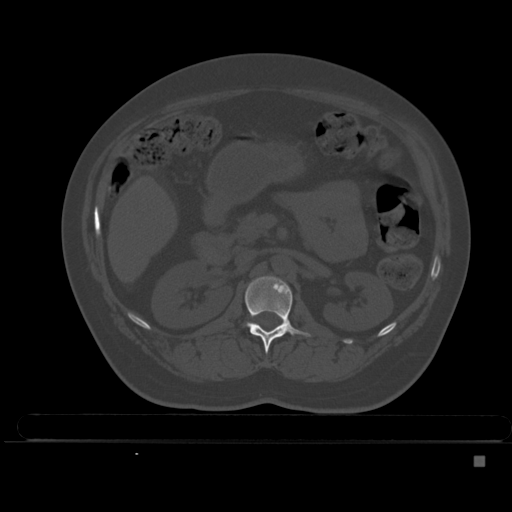
CT including the spine, one axial slice. Position 192 of 495 along the scan axis. Bone window (W 1800 / L 400 HU). 1.5 mm slice thickness. 512 × 512 image matrix. Female patient, age 33 years. From the clinical record (not read from this slice): primary cancer: breast; vertebrae with lytic lesions (as recorded): T1.
Annotated regions visible in this slice (semi-automatic segmentation, software-assisted and operator-edited):
- L1 vertebra: bounding box <244,276,311,353> (left, top, right, bottom; pixels)